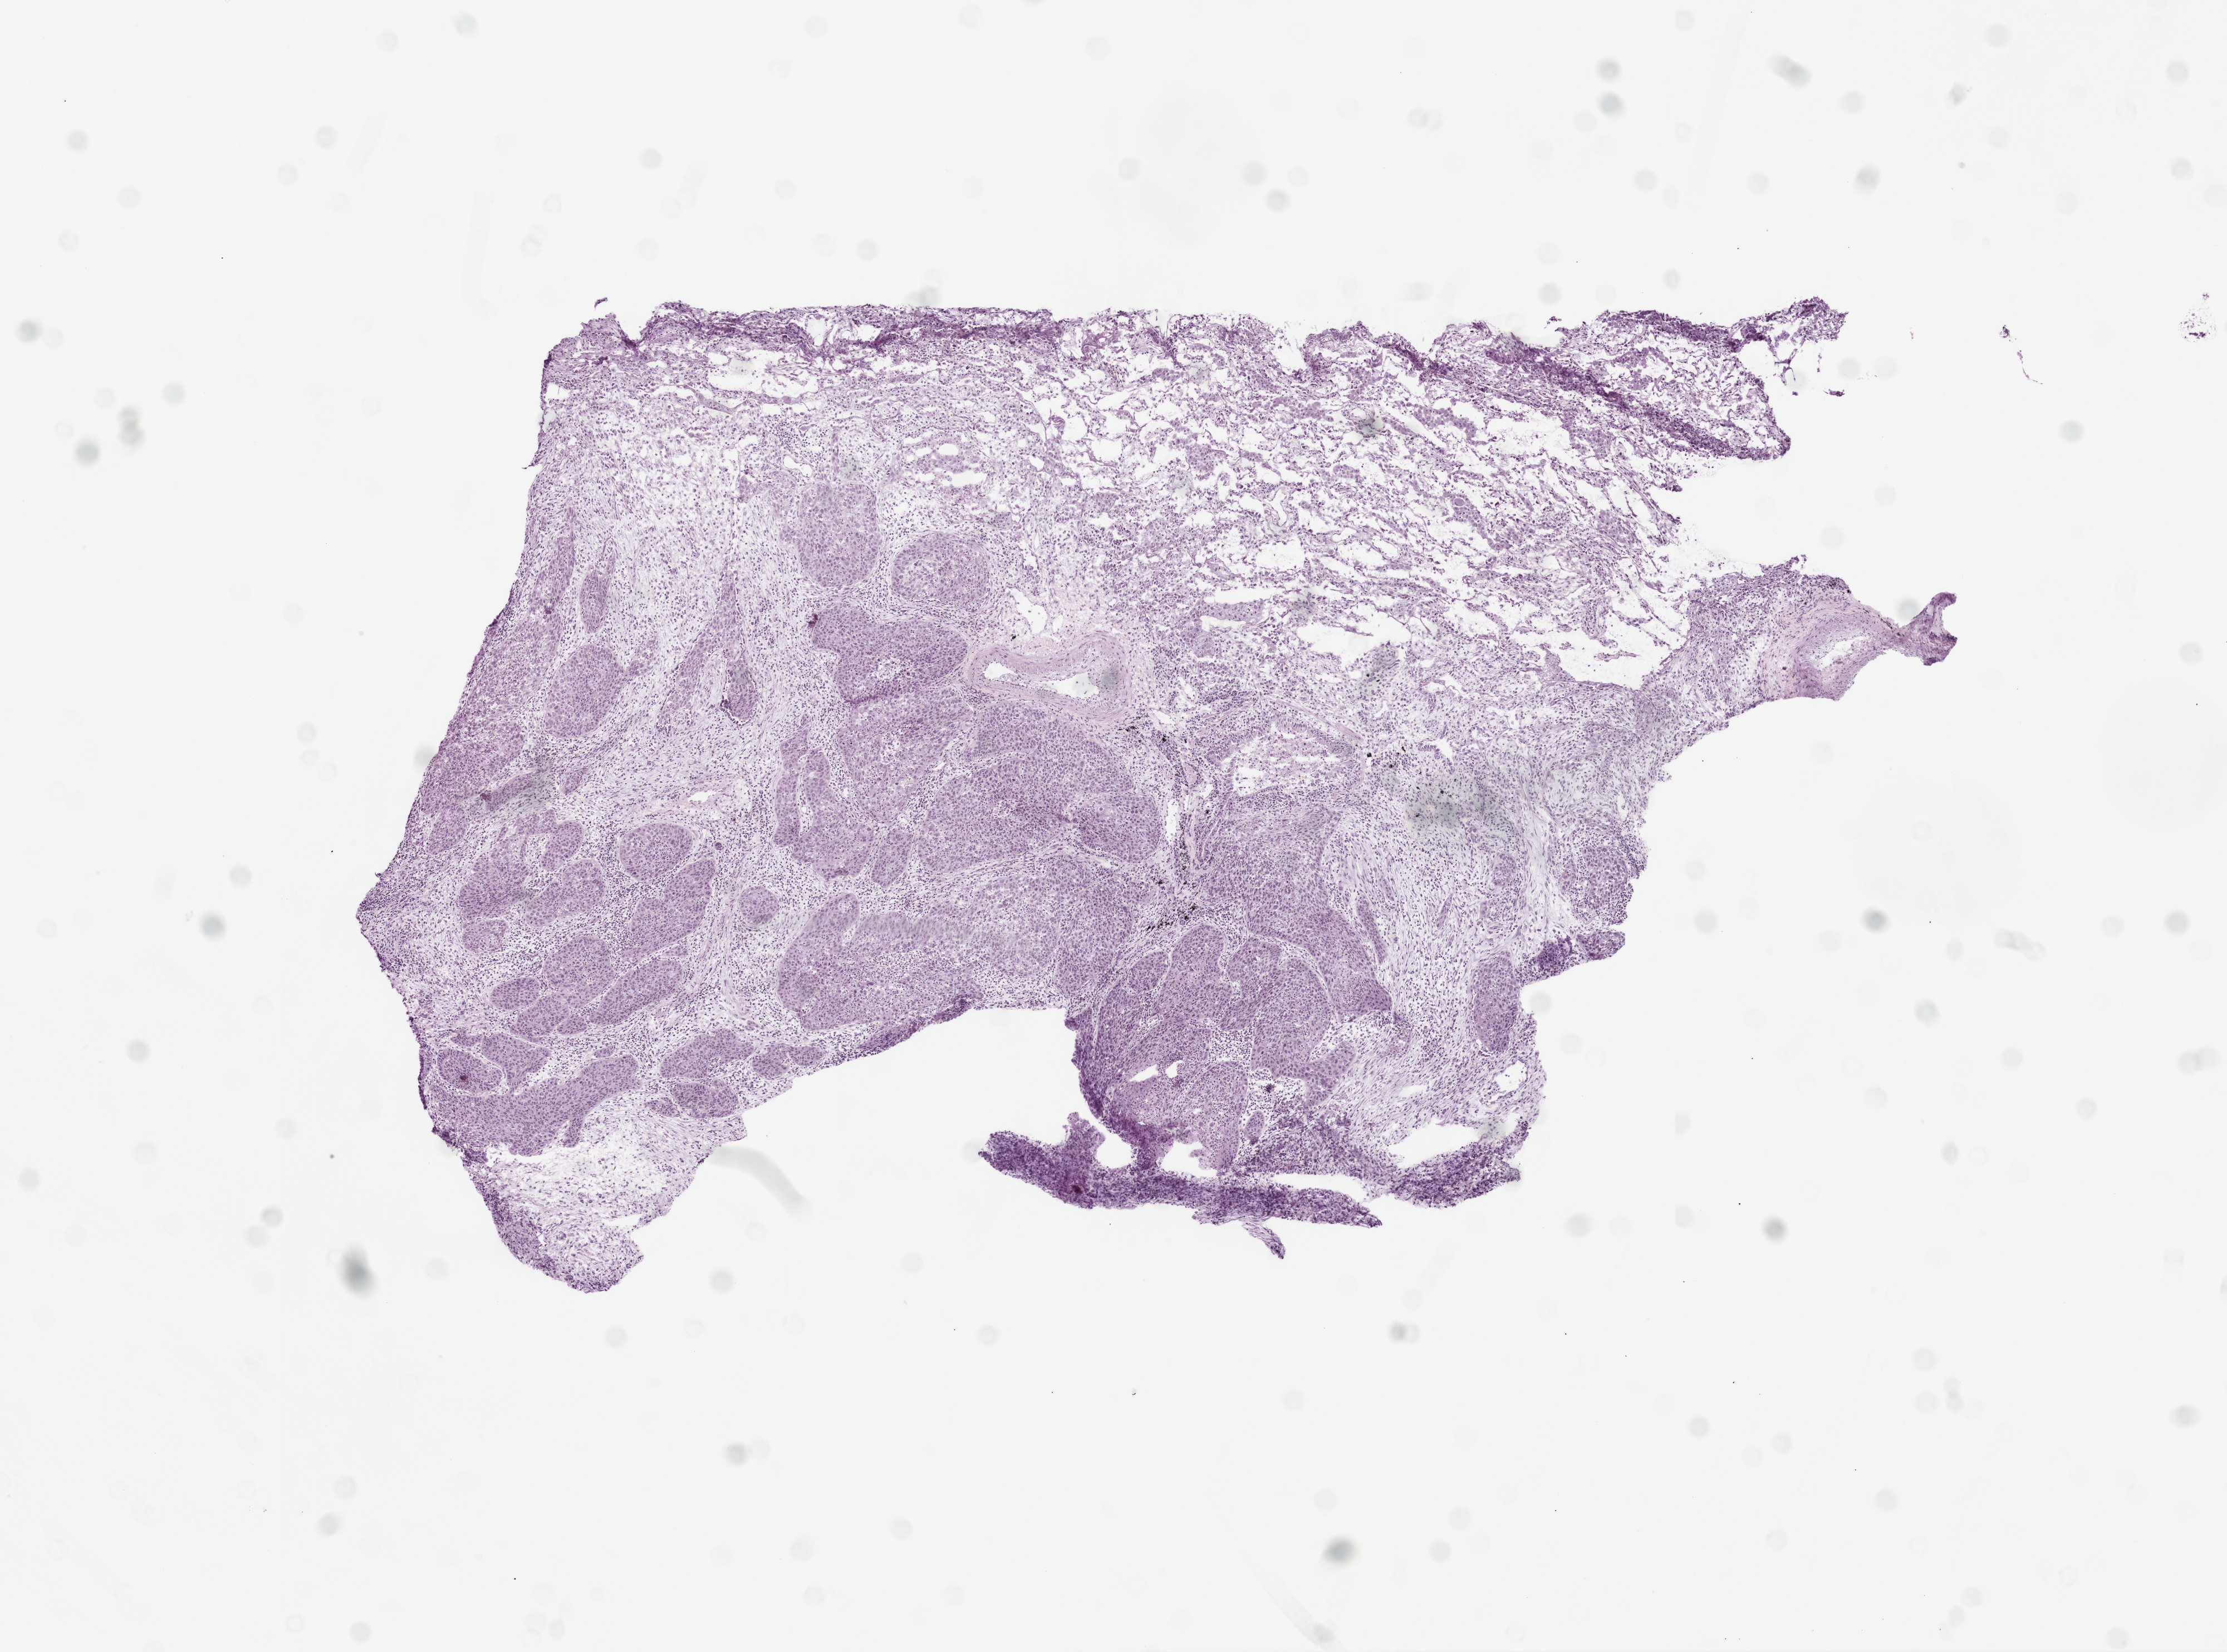
Digitized H&E tissue section (whole slide), a low-resolution overview of the entire scanned area, about 8.0 x 6.0 mm (acquisition: 20x scan). Frozen section. Lung, primary tumour sample. Male patient; age at initial diagnosis 74 years. Slide review estimates, as recorded: tumour cells 55%, tumour nuclei 60%, normal cells 20%, stromal cells 20%, necrosis 5%.
Pathologic diagnosis: Squamous cell carcinoma, NOS (upper lobe, lung). Laterality: left. AJCC pathologic stage: IB.